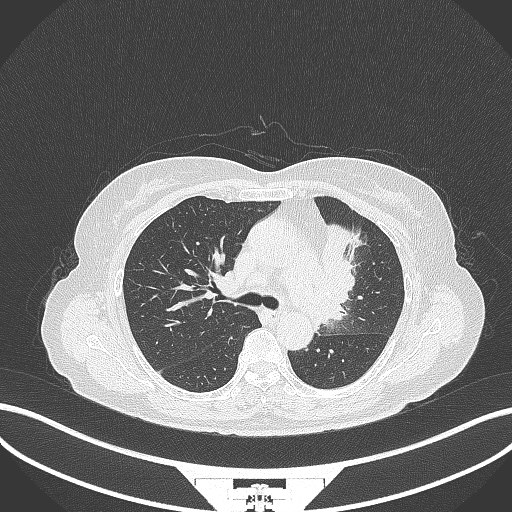
Chest CT, one axial slice; position 217 of 382 along the scan axis; reconstruction kernel B70f; 120 kVp; lung window (W 1500 / L -600 HU); 1 mm slice thickness; 512 × 512 image matrix, field of view 400 × 400 mm. Patient: female, 64 years. From the clinical record (not read from this slice): clinical TNM (as recorded): T2a N2 M0.
Structures marked on this image (bounding box drawn by a radiologist):
- lung tumour (recorded histology: adenocarcinoma): bounding box (x1, y1, x2, y2) in pixels: (319, 217, 362, 325)